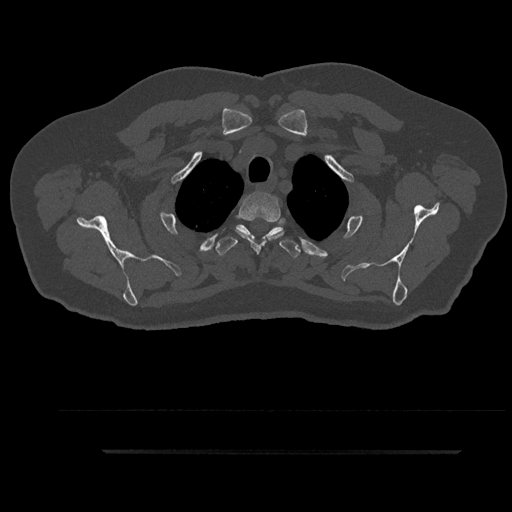
CT including the spine, one axial slice; position 742 of 797 along the scan axis; 120 kVp; bone window (W 1800 / L 400 HU); 0.5 mm slice thickness; 512 × 512 image matrix, field of view 432 × 432 mm. Patient: male, 63 years. From the clinical record (not read from this slice): primary cancer: renal.
Structures marked on this image (semi-automatically segmented with operator editing):
- T2 vertebra: bounding box <236,191,284,253> (left, top, right, bottom; pixels)
- T3 vertebra: <214,224,301,258>